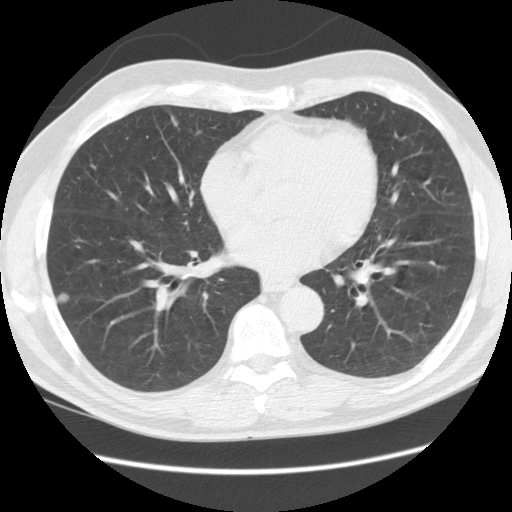
Low-dose screening chest CT, one axial slice. Position 42 of 111 along the scan axis. Reconstruction kernel STANDARD. Lung window (W 1500 / L -600 HU). 2.5 mm slice thickness. 512 × 512 image matrix, field of view 370 × 370 mm.
Annotated regions visible in this slice (outlined manually by an expert reader):
- lesion 2 (nodule, lower lobe of right lung): box from (x=58, y=293) to (x=69, y=303) px